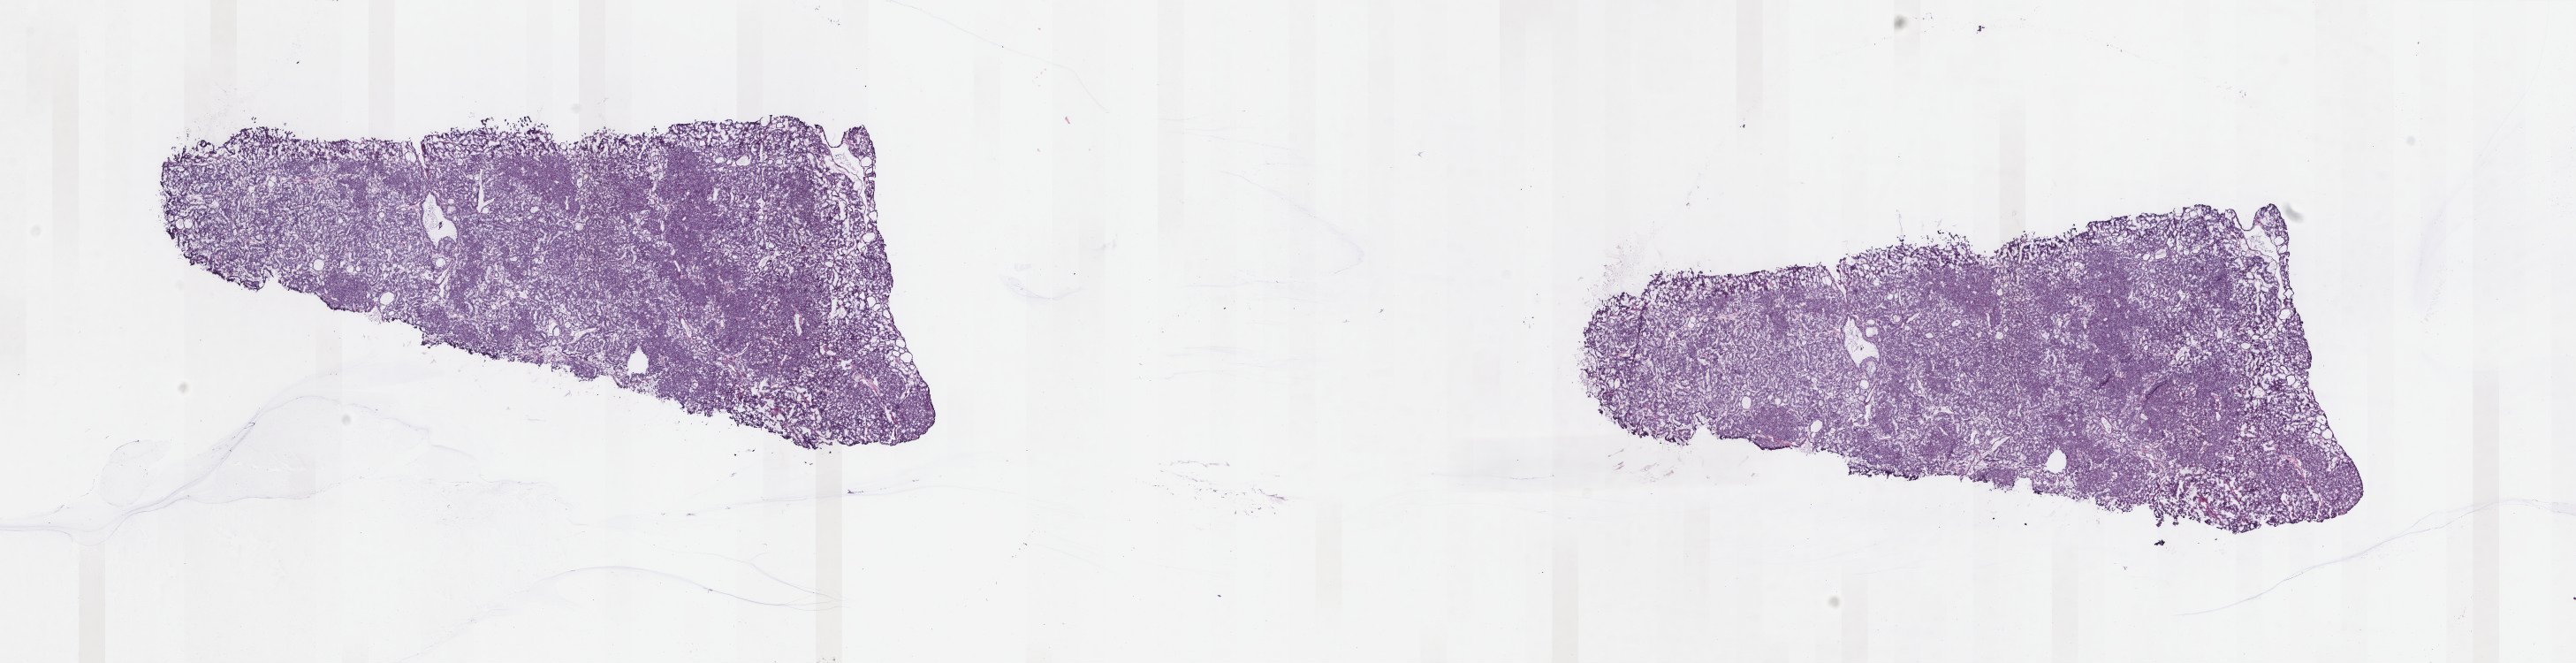
Digitized Hematoxylin and eosin (H&E) stained tissue section (whole slide) — a low-resolution overview of the entire scanned area, about 23.1 x 6.0 mm (acquisition: 40x scan). Frozen section. Sample: primary tumour, thyroid. Female, age 23 years at initial diagnosis. Composition of this section per pathologist review: tumour cells 100%, tumour nuclei 95%, normal cells 0%, stromal cells 0%, necrosis 0%. Inflammatory infiltration, as recorded: lymphocyte infiltration 0%, monocyte infiltration 0%, neutrophil infiltration 0%.
Histologic diagnosis: Papillary carcinoma, follicular variant. AJCC pathologic stage: I. Laterality: left.